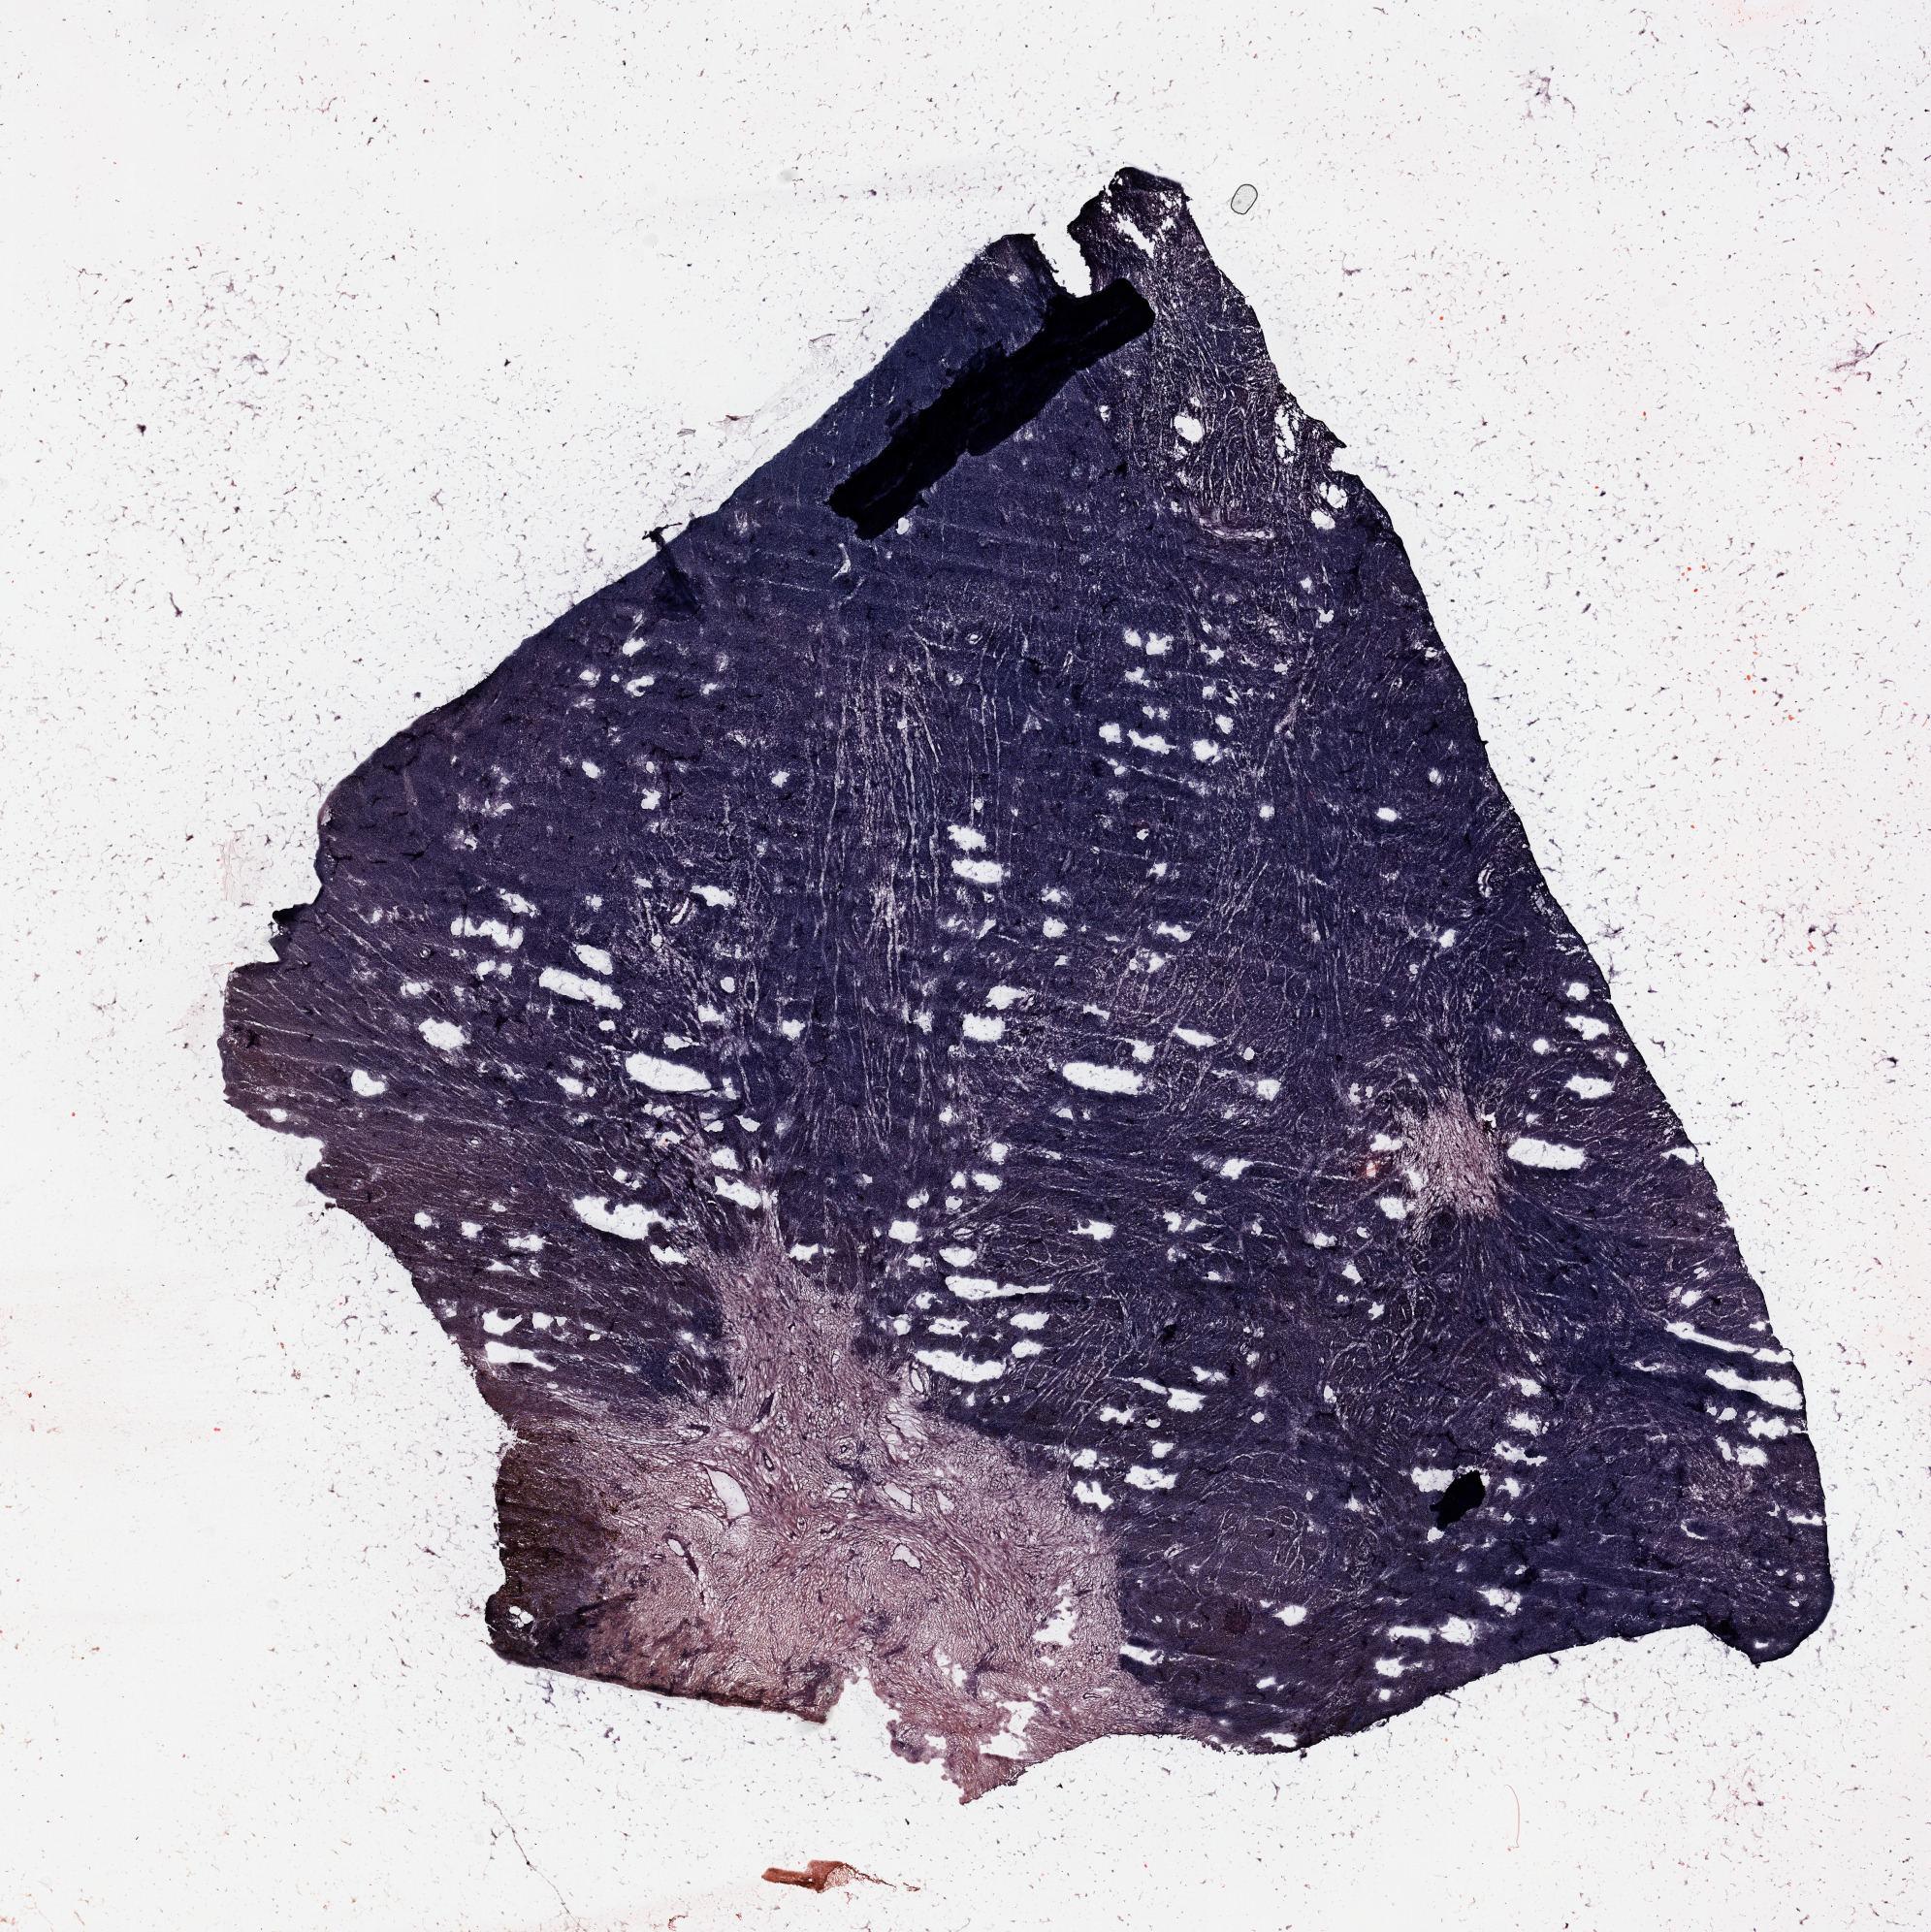
H&E-stained whole-slide image — whole scanned area (about 15.8 x 15.8 mm) shown as a low-resolution overview. Melanoma tumour tissue; sampled site not recorded. 67-year-old female patient.
Patient diagnosis (cohort enrolment): cutaneous melanoma (skin). Primary tumour site (as recorded): extremities.